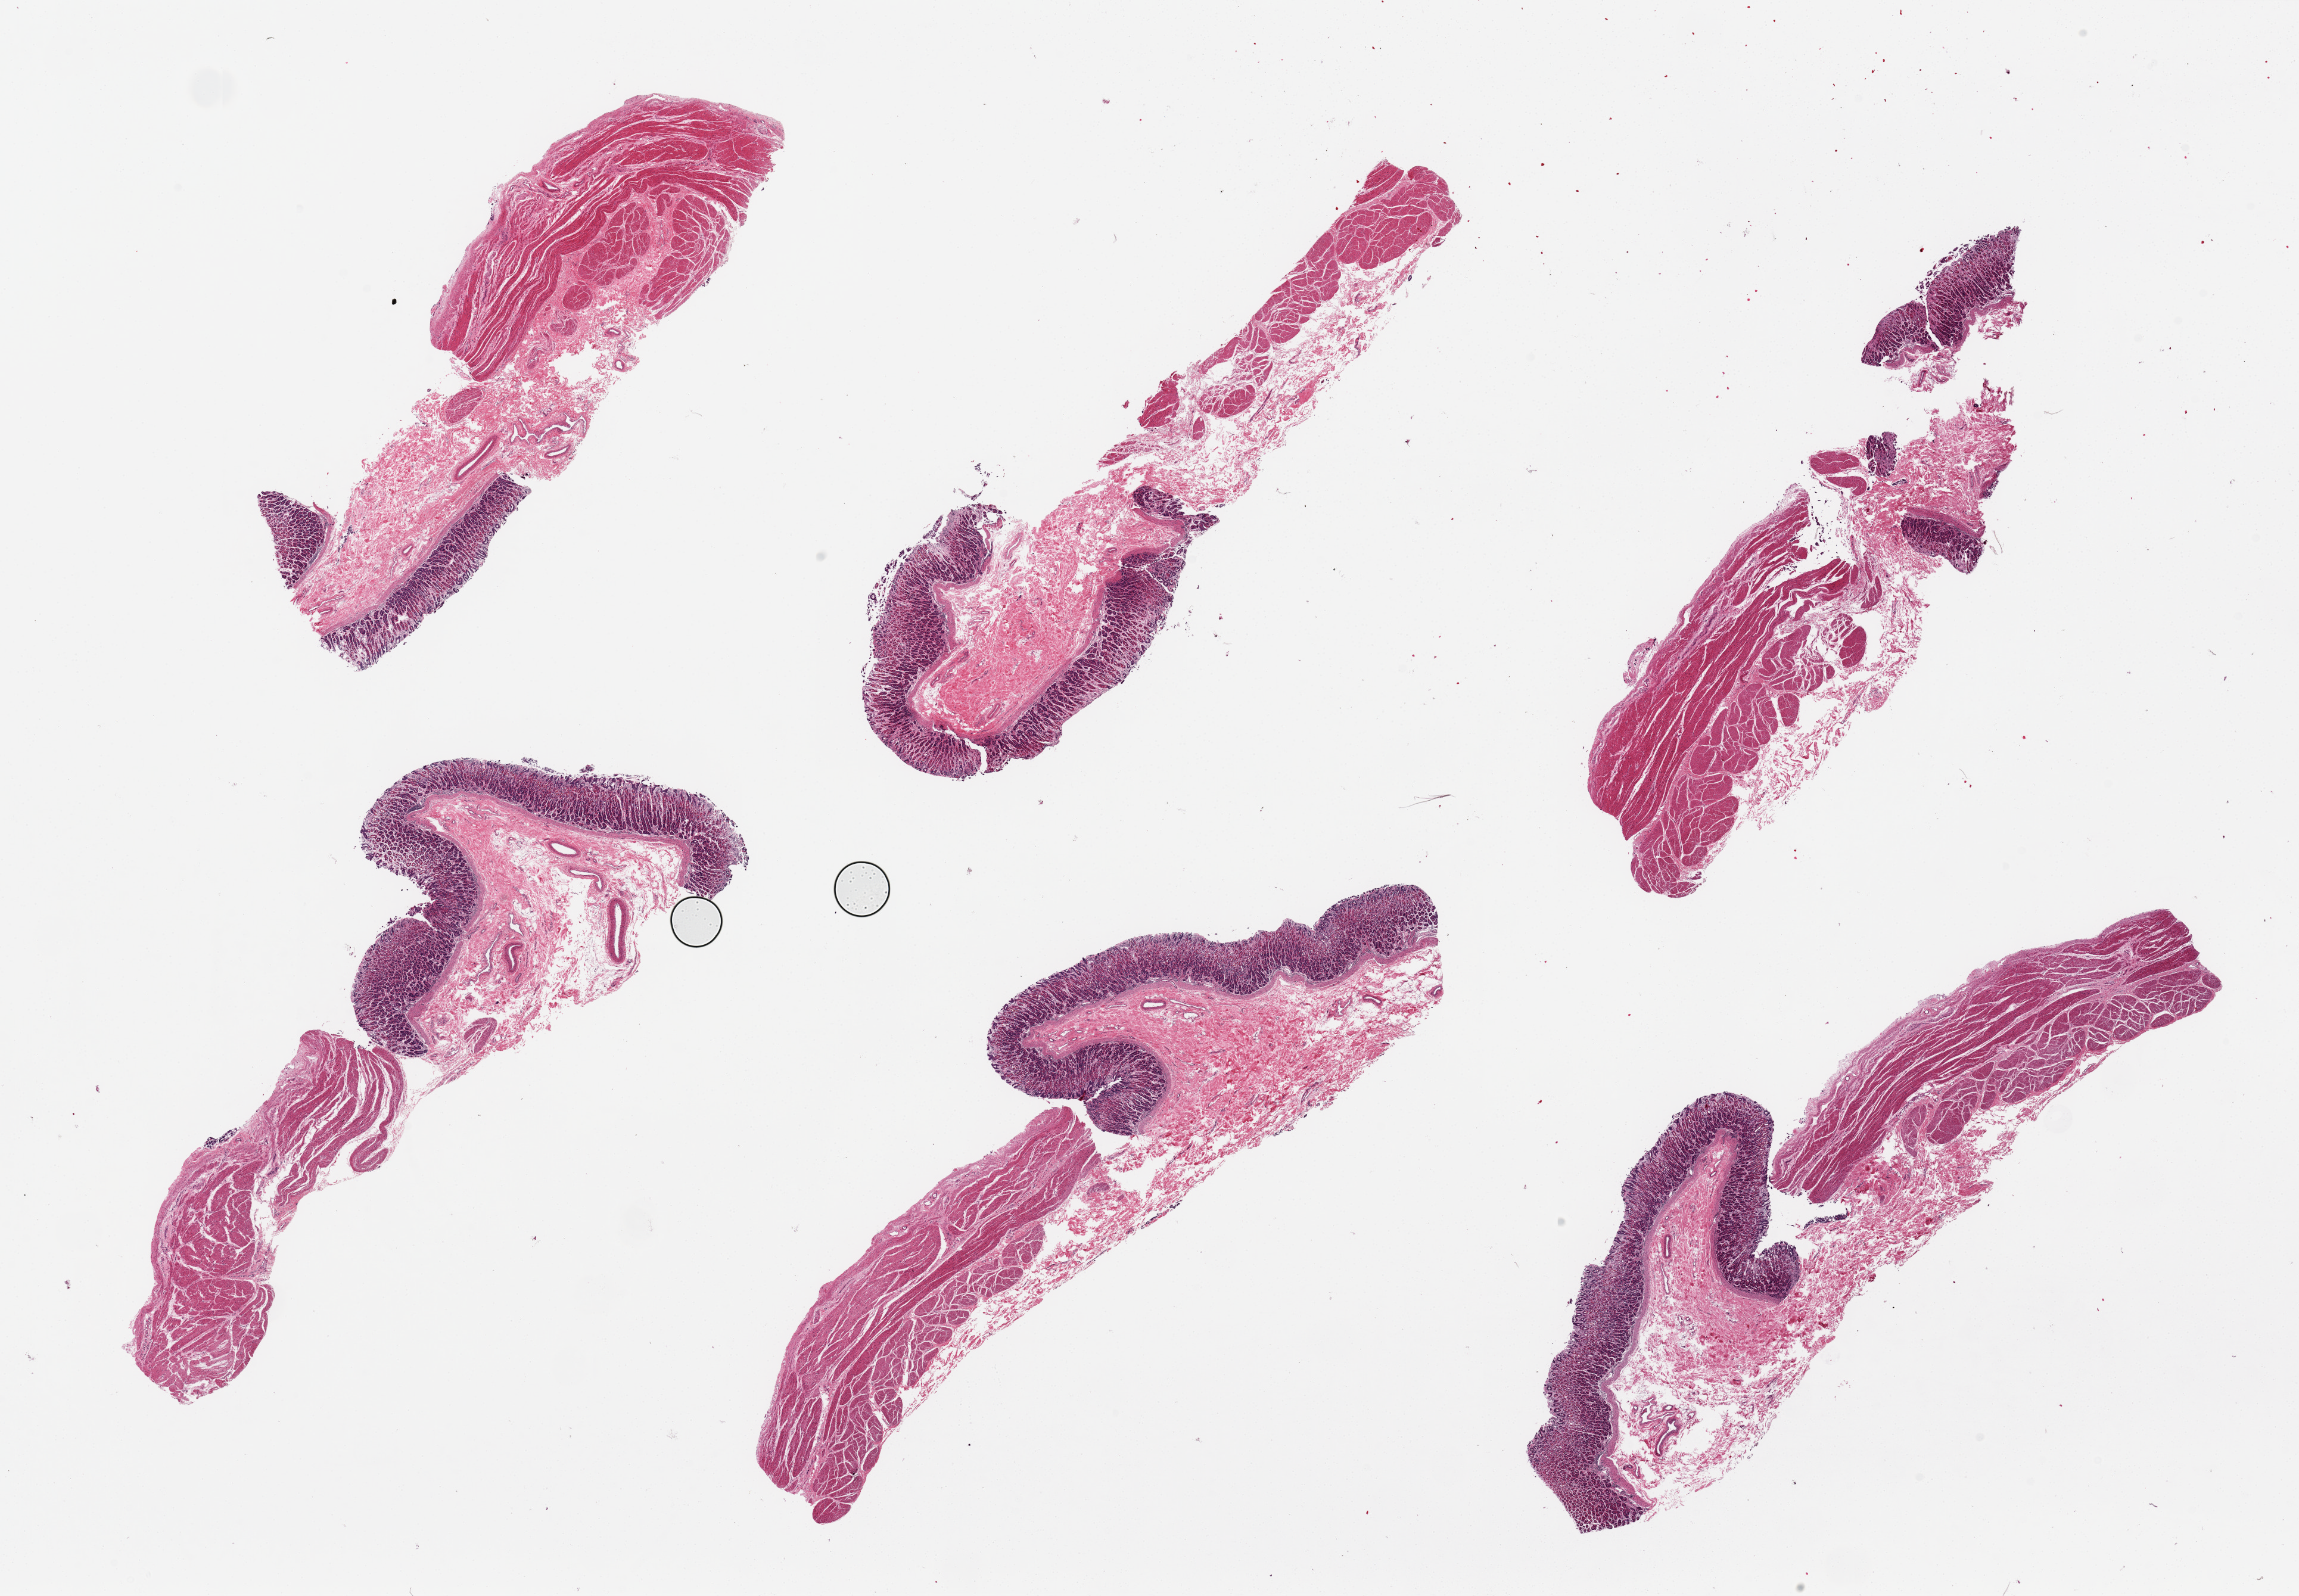
Digitized haematoxylin and eosin-stained section, brightfield — low-resolution overview of the scanned area, about 30.5 x 21.2 mm (from a 20x scan), PAXgene-fixed, paraffin-embedded tissue, section of stomach (target tissue), tissue donor sample. Donor: male.
• reviewer comment on this tissue sample: 6 pieces; surface autolysis; mucosa and muscularis sampled